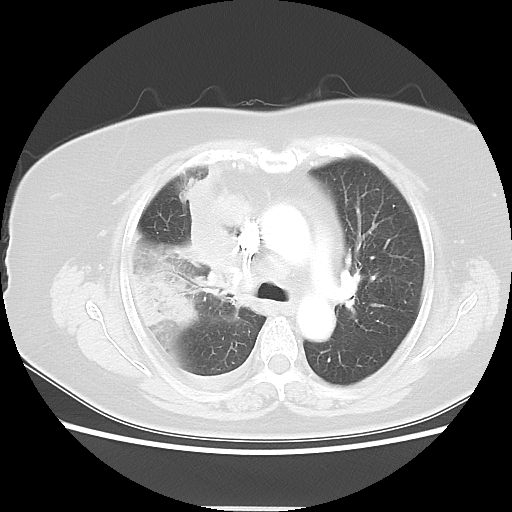
Chest CT, one axial slice. Position 32 of 48 along the scan axis. 120 kVp. Lung window (W 1500 / L -600 HU). 5 mm slice thickness. 512 × 512 image matrix, field of view 360 × 360 mm. Patient: female, 73 years. Case-level facts recorded for this patient, not image findings: clinical TNM (as recorded): T3 N3 M1b; histopathological grade: G3.
Structures marked on this image (bounding box drawn by a radiologist):
- lung tumour (recorded histology: small cell carcinoma): bounding box <178,165,257,297> (left, top, right, bottom; pixels)